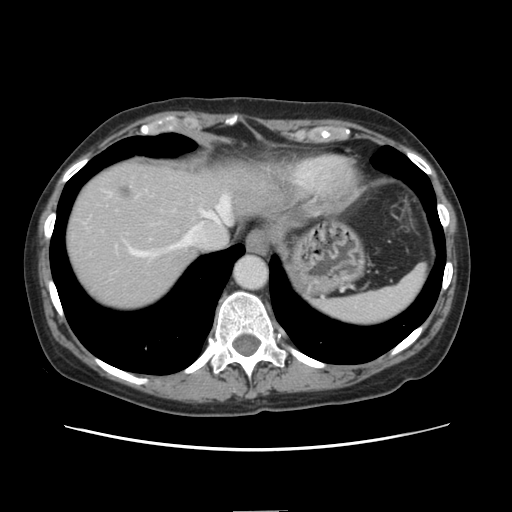
Contrast-enhanced abdominal CT, one axial slice; position 121 of 141 along the scan axis; intravenous contrast given; soft-tissue window (W 400 / L 40 HU); 512 × 512 image matrix, field of view 350 × 350 mm. Female patient, age 63 years. From the clinical record (not read from this slice): diagnosis: colorectal cancer liver metastases, imaged before liver resection; multiple liver metastases: yes.
Structures marked on this image (outlined manually by an expert reader):
- hepatic veins: bounding box [x1, y1, x2, y2] px = [129, 196, 230, 258]
- liver: [66, 160, 297, 312]
- planned liver remnant (the part of the liver to remain after resection): [205, 165, 273, 227]